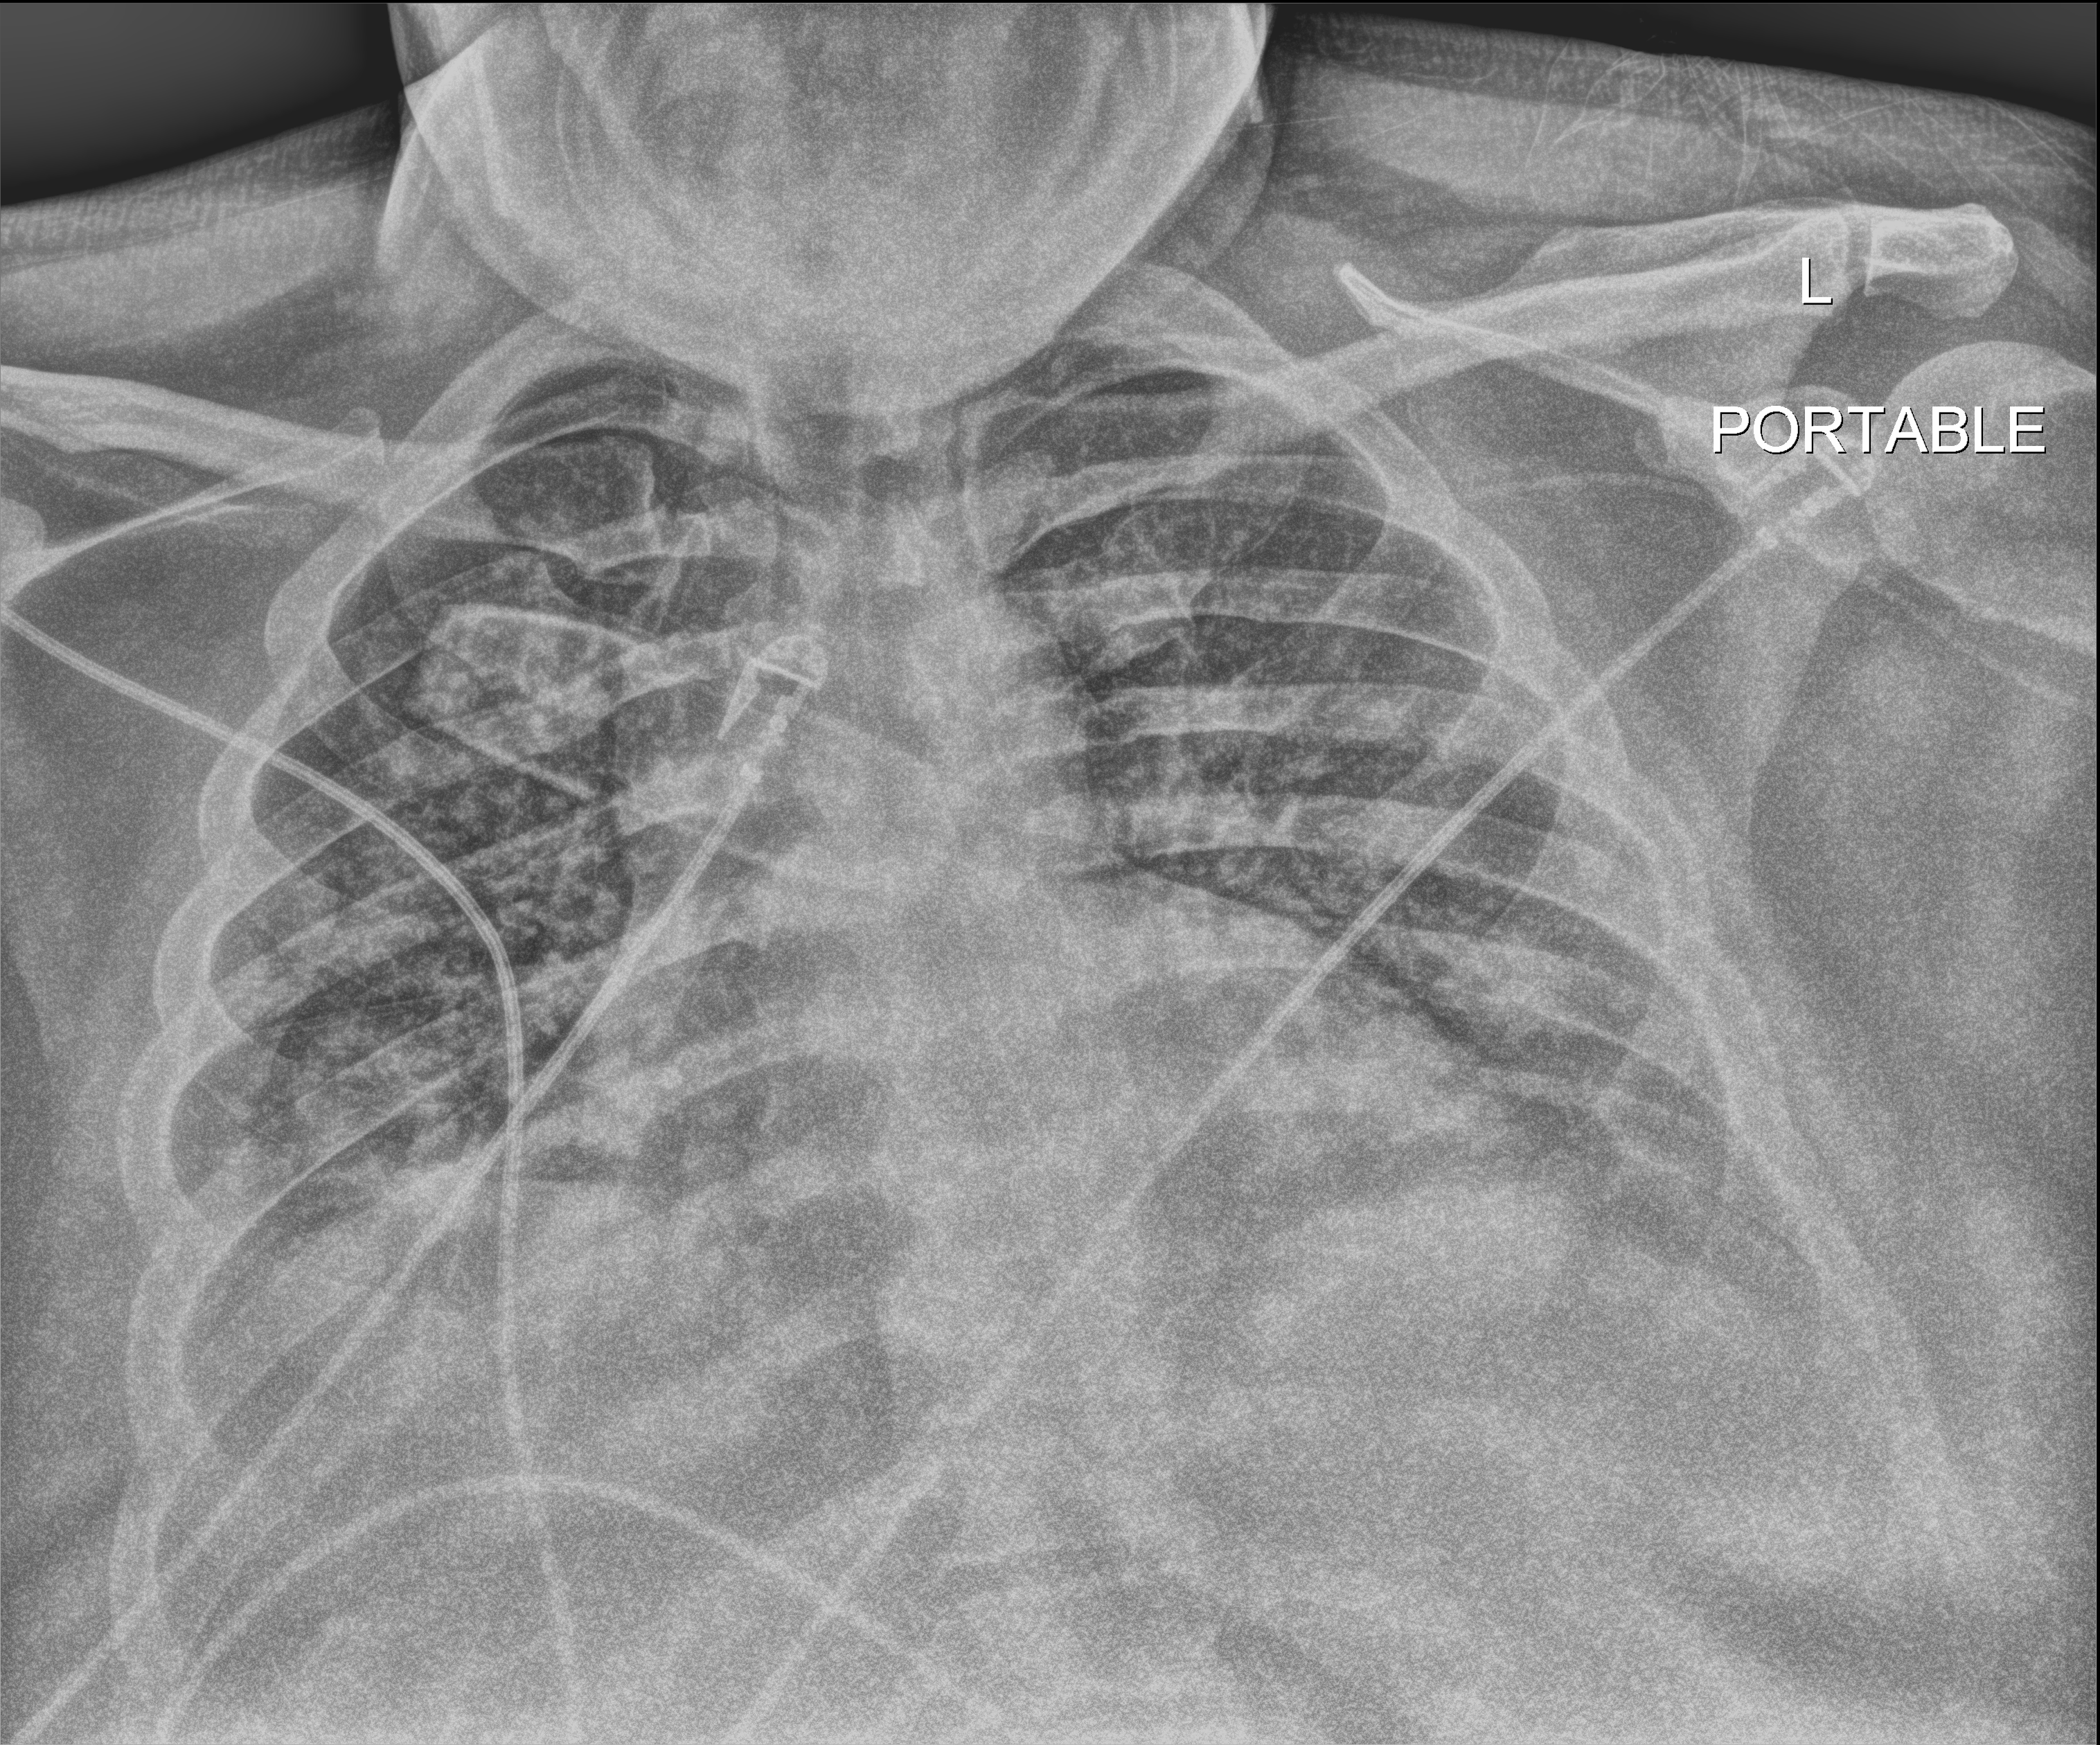
Chest X-ray (portable), anteroposterior (AP) projection. Male patient hospitalised with COVID-19, age 18–59 years.
From the hospital-stay record, not from the radiograph (when in the stay this image was taken is not recorded):
- admitted to intensive care during this hospital stay: yes
- mechanically ventilated during this hospital stay: no
- length of hospital stay: 19 days